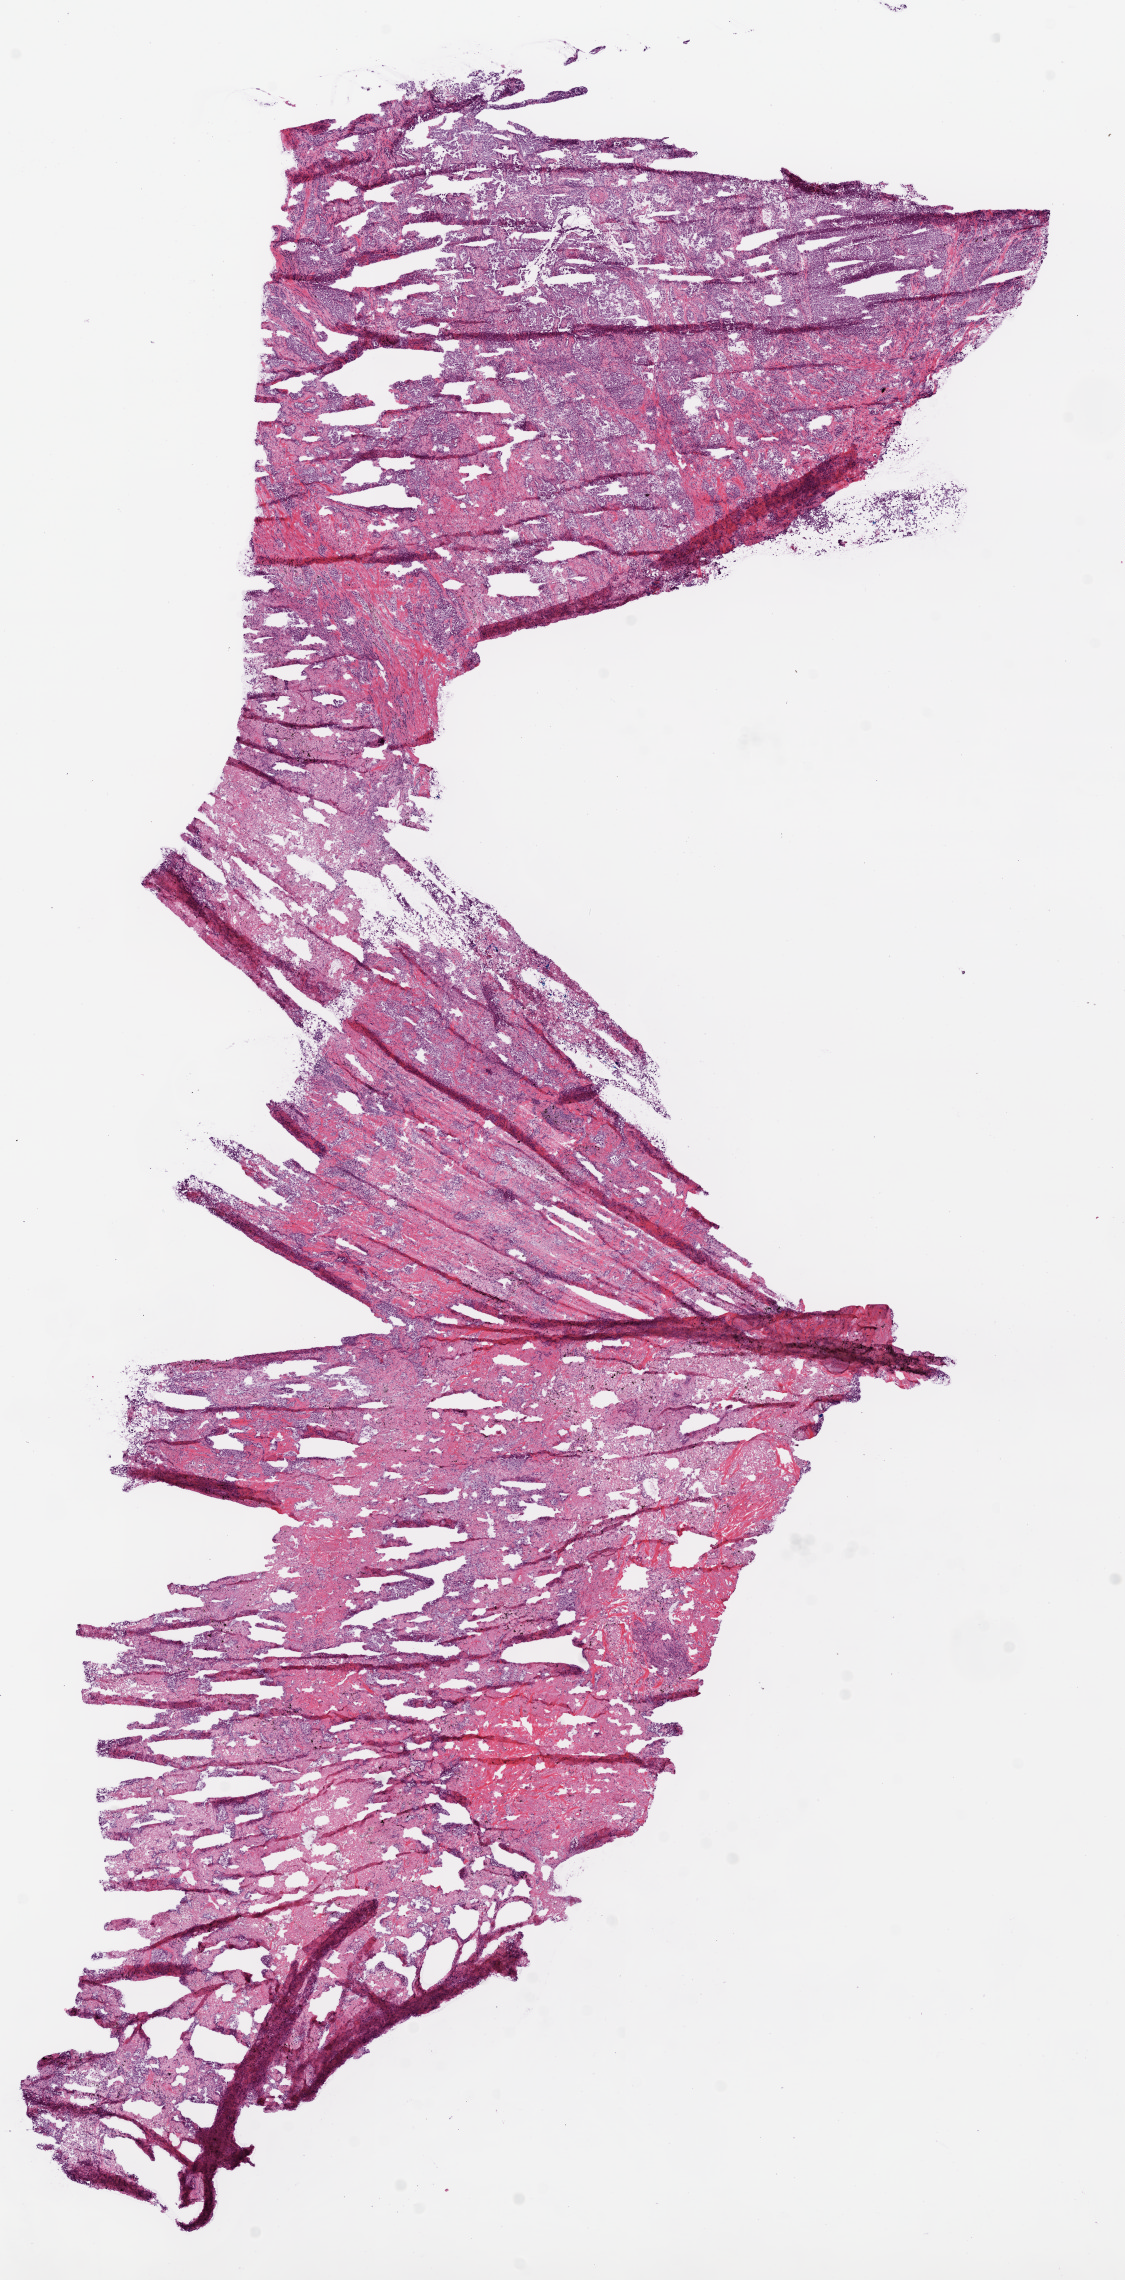
H&E-stained whole-slide image, low-resolution overview of the scanned area, about 9.0 x 18.3 mm (slide scanned at 20x); frozen section from the top of the tissue portion; primary tumour sample from the lung. Female, age 60 years at initial diagnosis. Composition of this section per pathologist review: tumour cells 60%, tumour nuclei 80%, normal cells 0%, stromal cells 35%, necrosis 5%.
Pathologic diagnosis: Adenocarcinoma, NOS. AJCC pathologic stage: IB (6th edition).